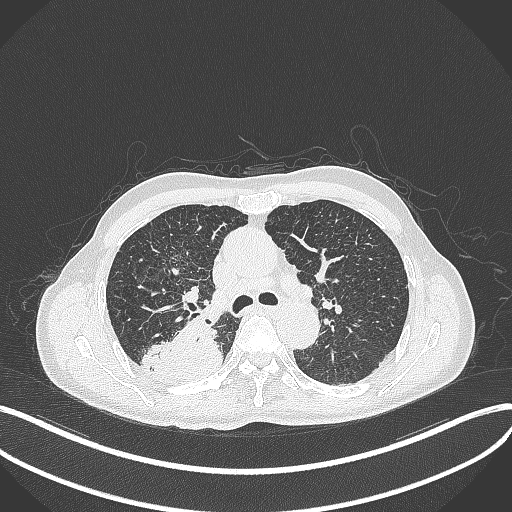
Chest CT, one axial slice. Slice 300 of 428 in the series (ordered by position). Reconstruction kernel B70f. Lung window (W 1500 / L -600 HU). 1 mm slice thickness. 512 × 512 image matrix, field of view 400 × 400 mm. Patient: male, 79 years. Case-level facts recorded for this patient, not image findings: clinical TNM (as recorded): T3 N0 M0.
Structures marked on this image (bounding box drawn by a radiologist):
- lung tumour (recorded histology: adenocarcinoma): bounding box (x1, y1, x2, y2) in pixels: (140, 313, 225, 378)